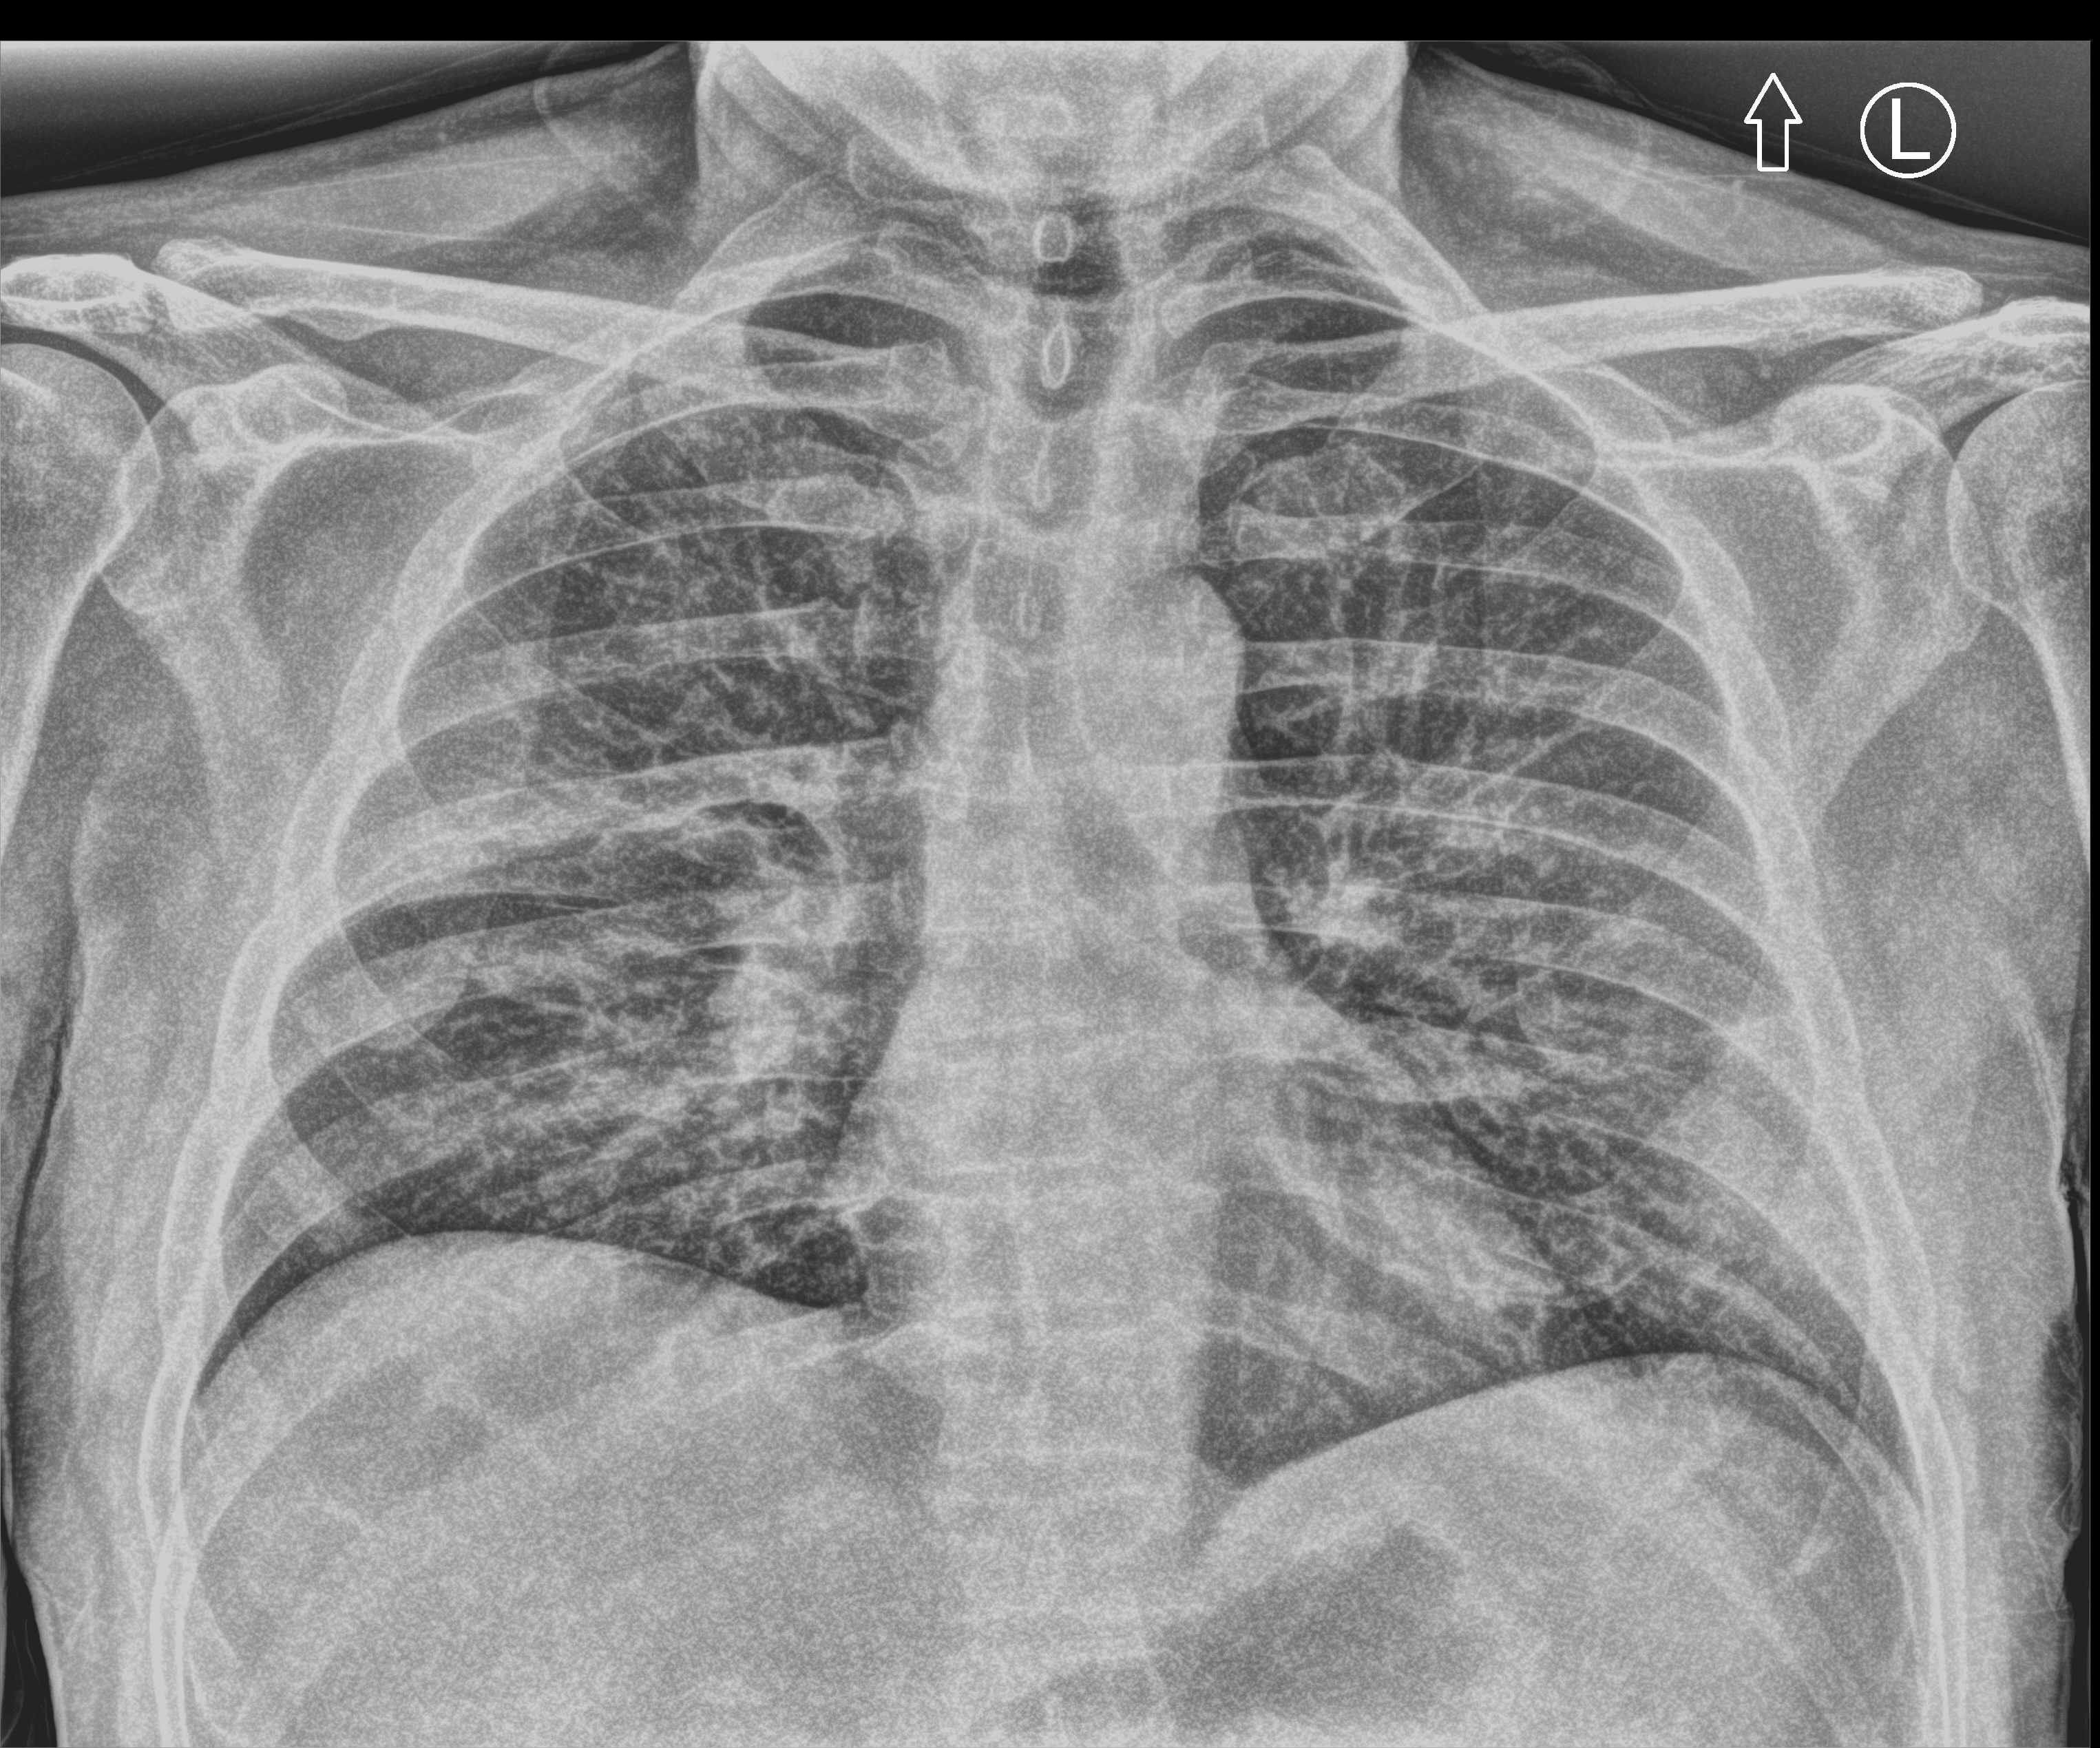
Chest X-ray (portable); anteroposterior (AP) projection. Male patient hospitalised with COVID-19, age 18–59 years.
From the hospital-stay record, not from the radiograph (when in the stay this image was taken is not recorded):
- admitted to intensive care during this hospital stay: no
- length of hospital stay: 11 days
- smoking status (admission record): former